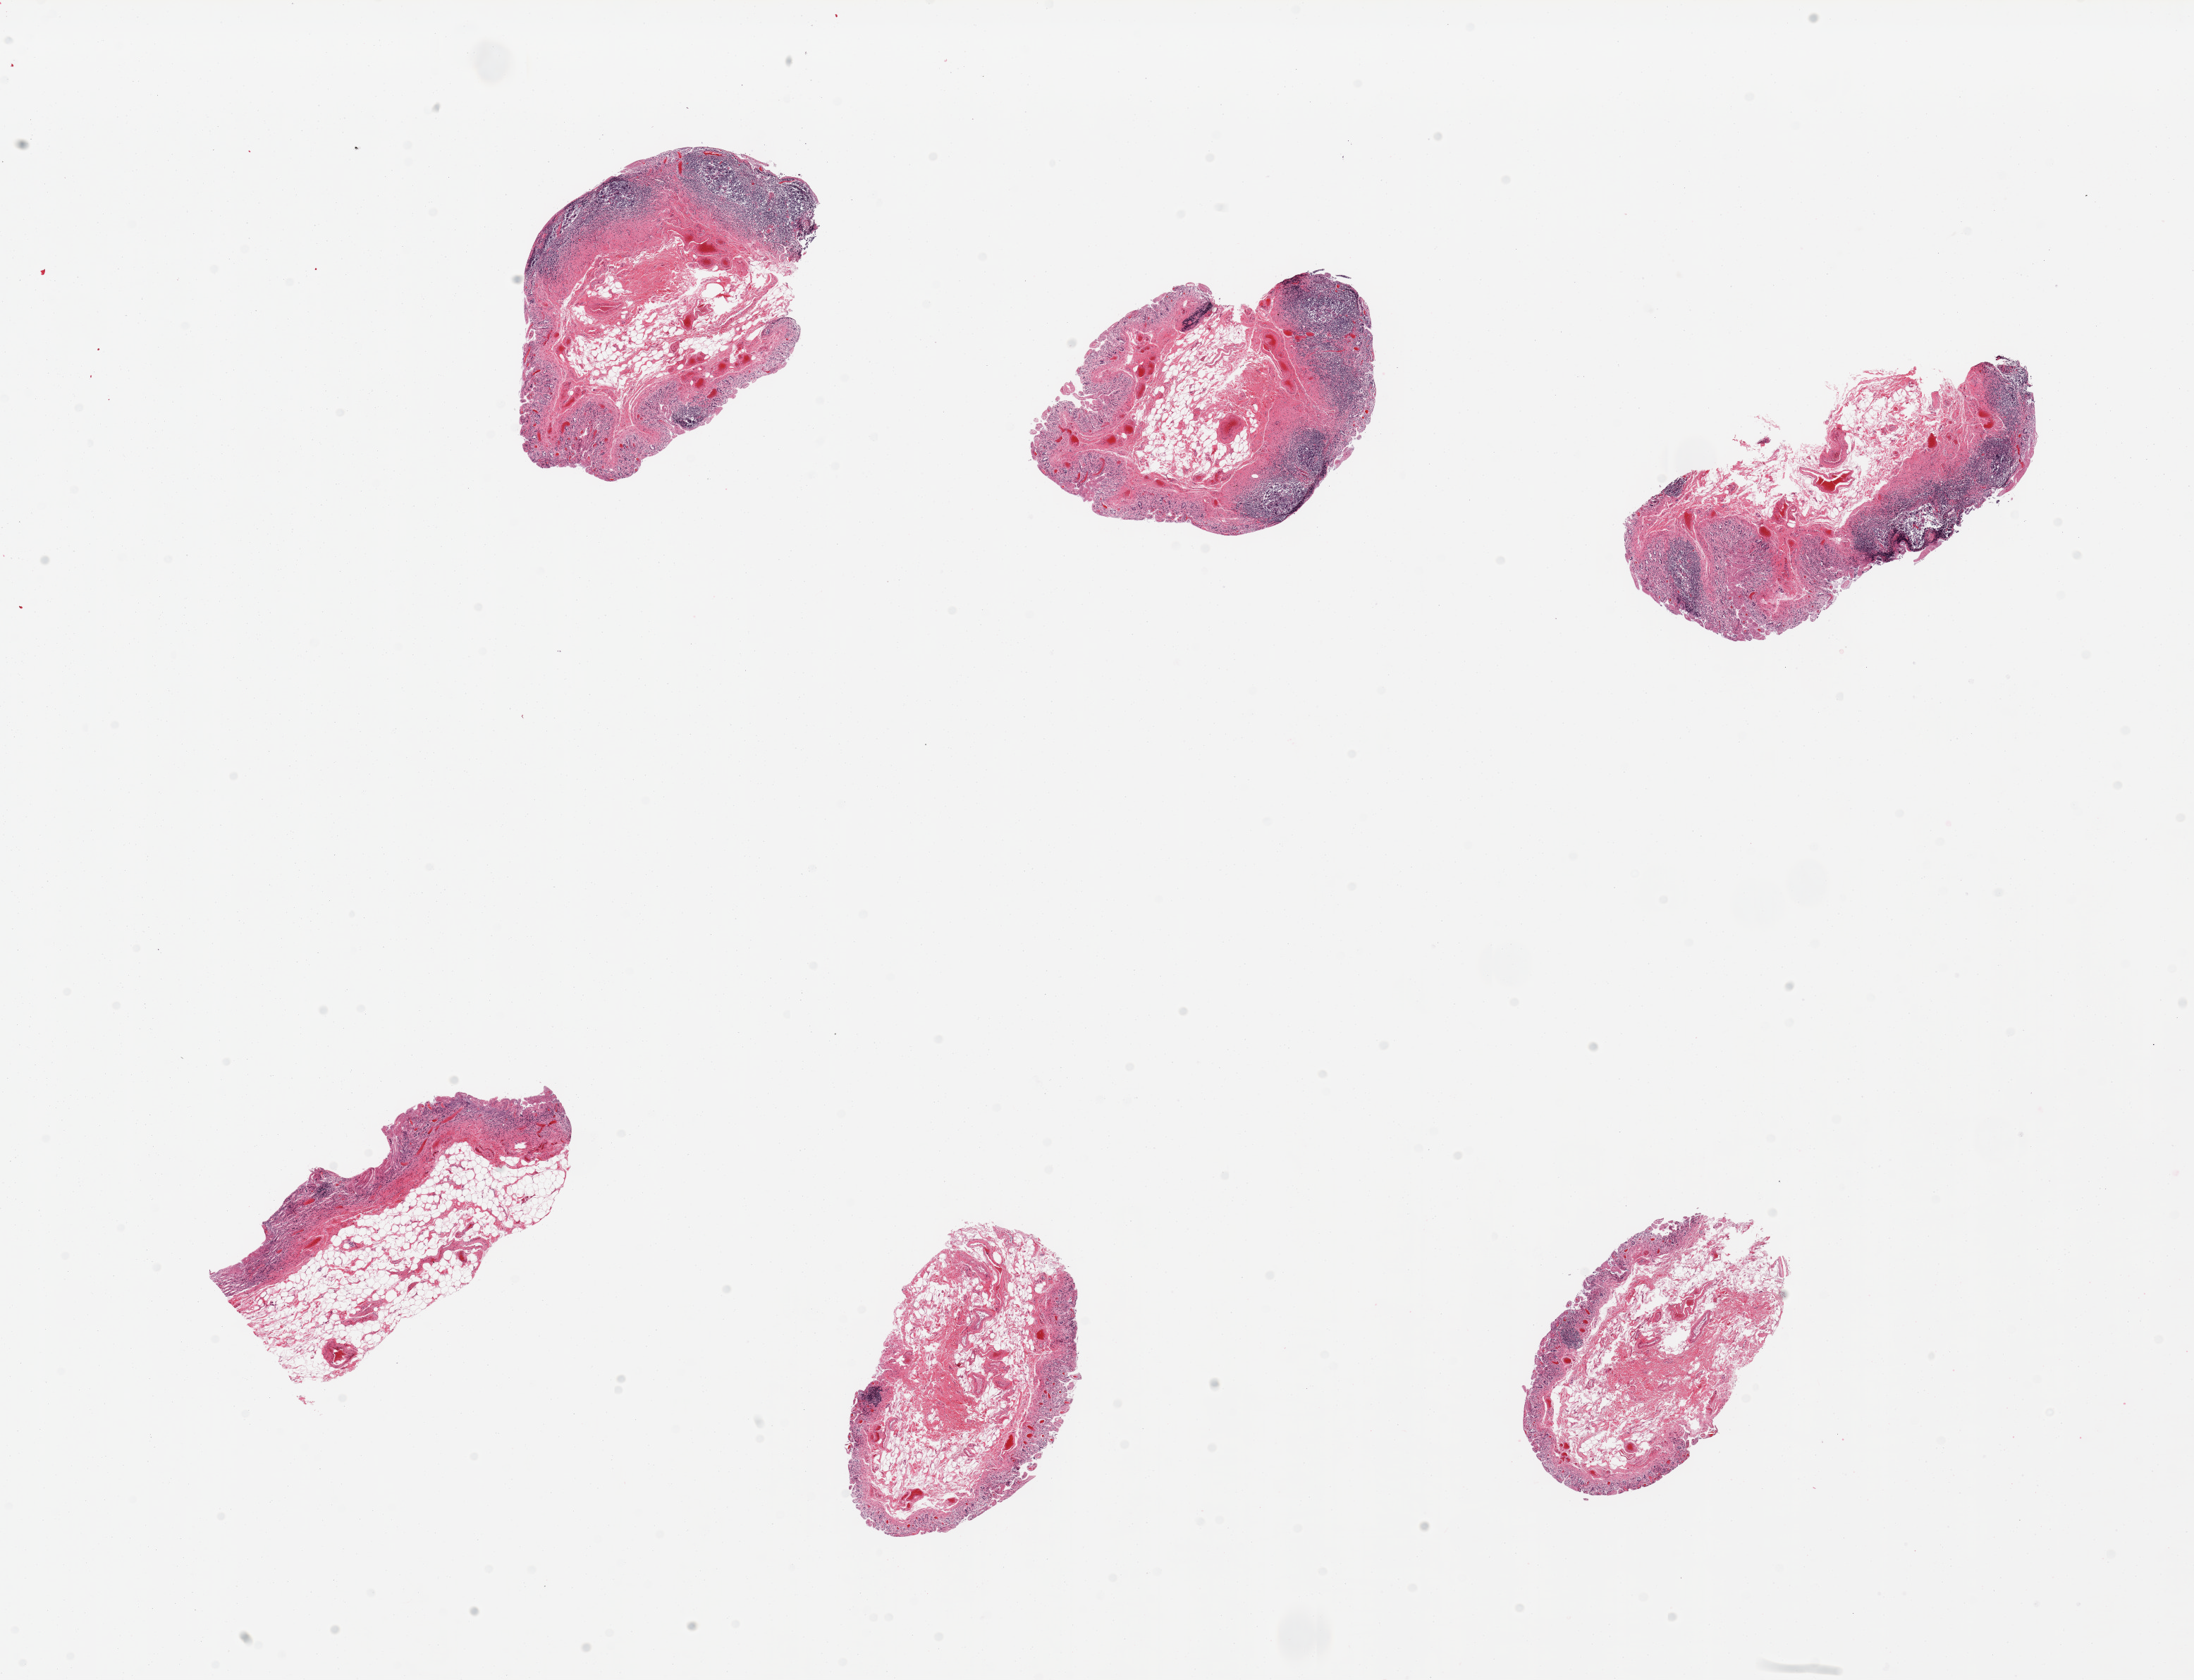
Digitized hematoxylin and eosin (H&E)-stained section — shown as a low-resolution overview of the whole scanned area (about 24.6 x 18.8 mm, acquisition: 20x scan). PAXgene-fixed paraffin-embedded (PFPE) section. Section of ileum (target tissue). Tissue donor sample. Donor sex: male.
* pathologist's review note for this sample: 6 pieces, mucsoa autolyzed, lymphoid/Peyer aggregates are !20% total tissue